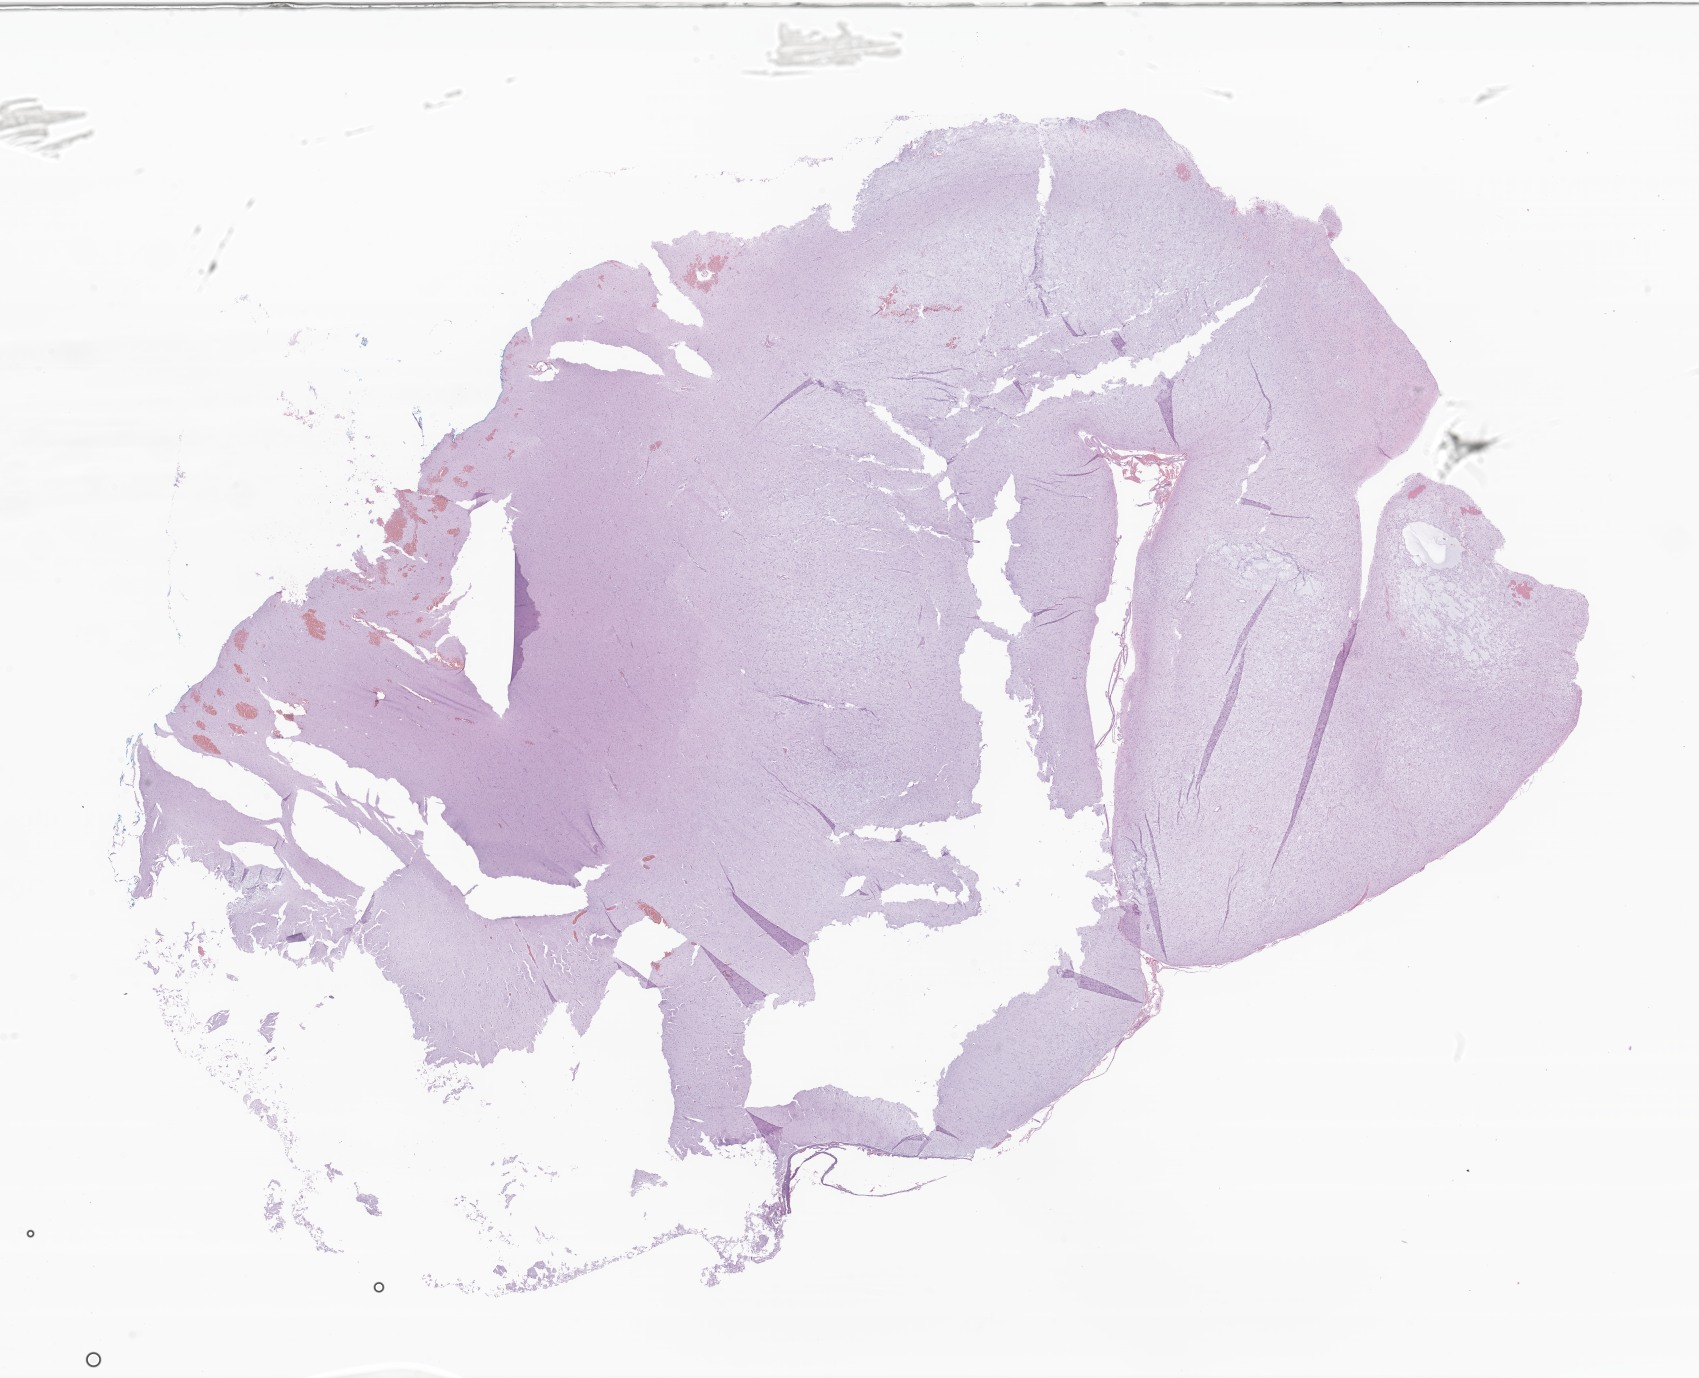
H&E whole-slide image of tumor tissue from the frontal lobe — whole scanned area (about 28.7 x 23.2 mm) shown as a low-resolution overview. Formalin-fixed paraffin-embedded section. Patient male; age 194 months (16 years 2 months).
Diagnosis: Dysembryoplastic neuroepithelial tumor.